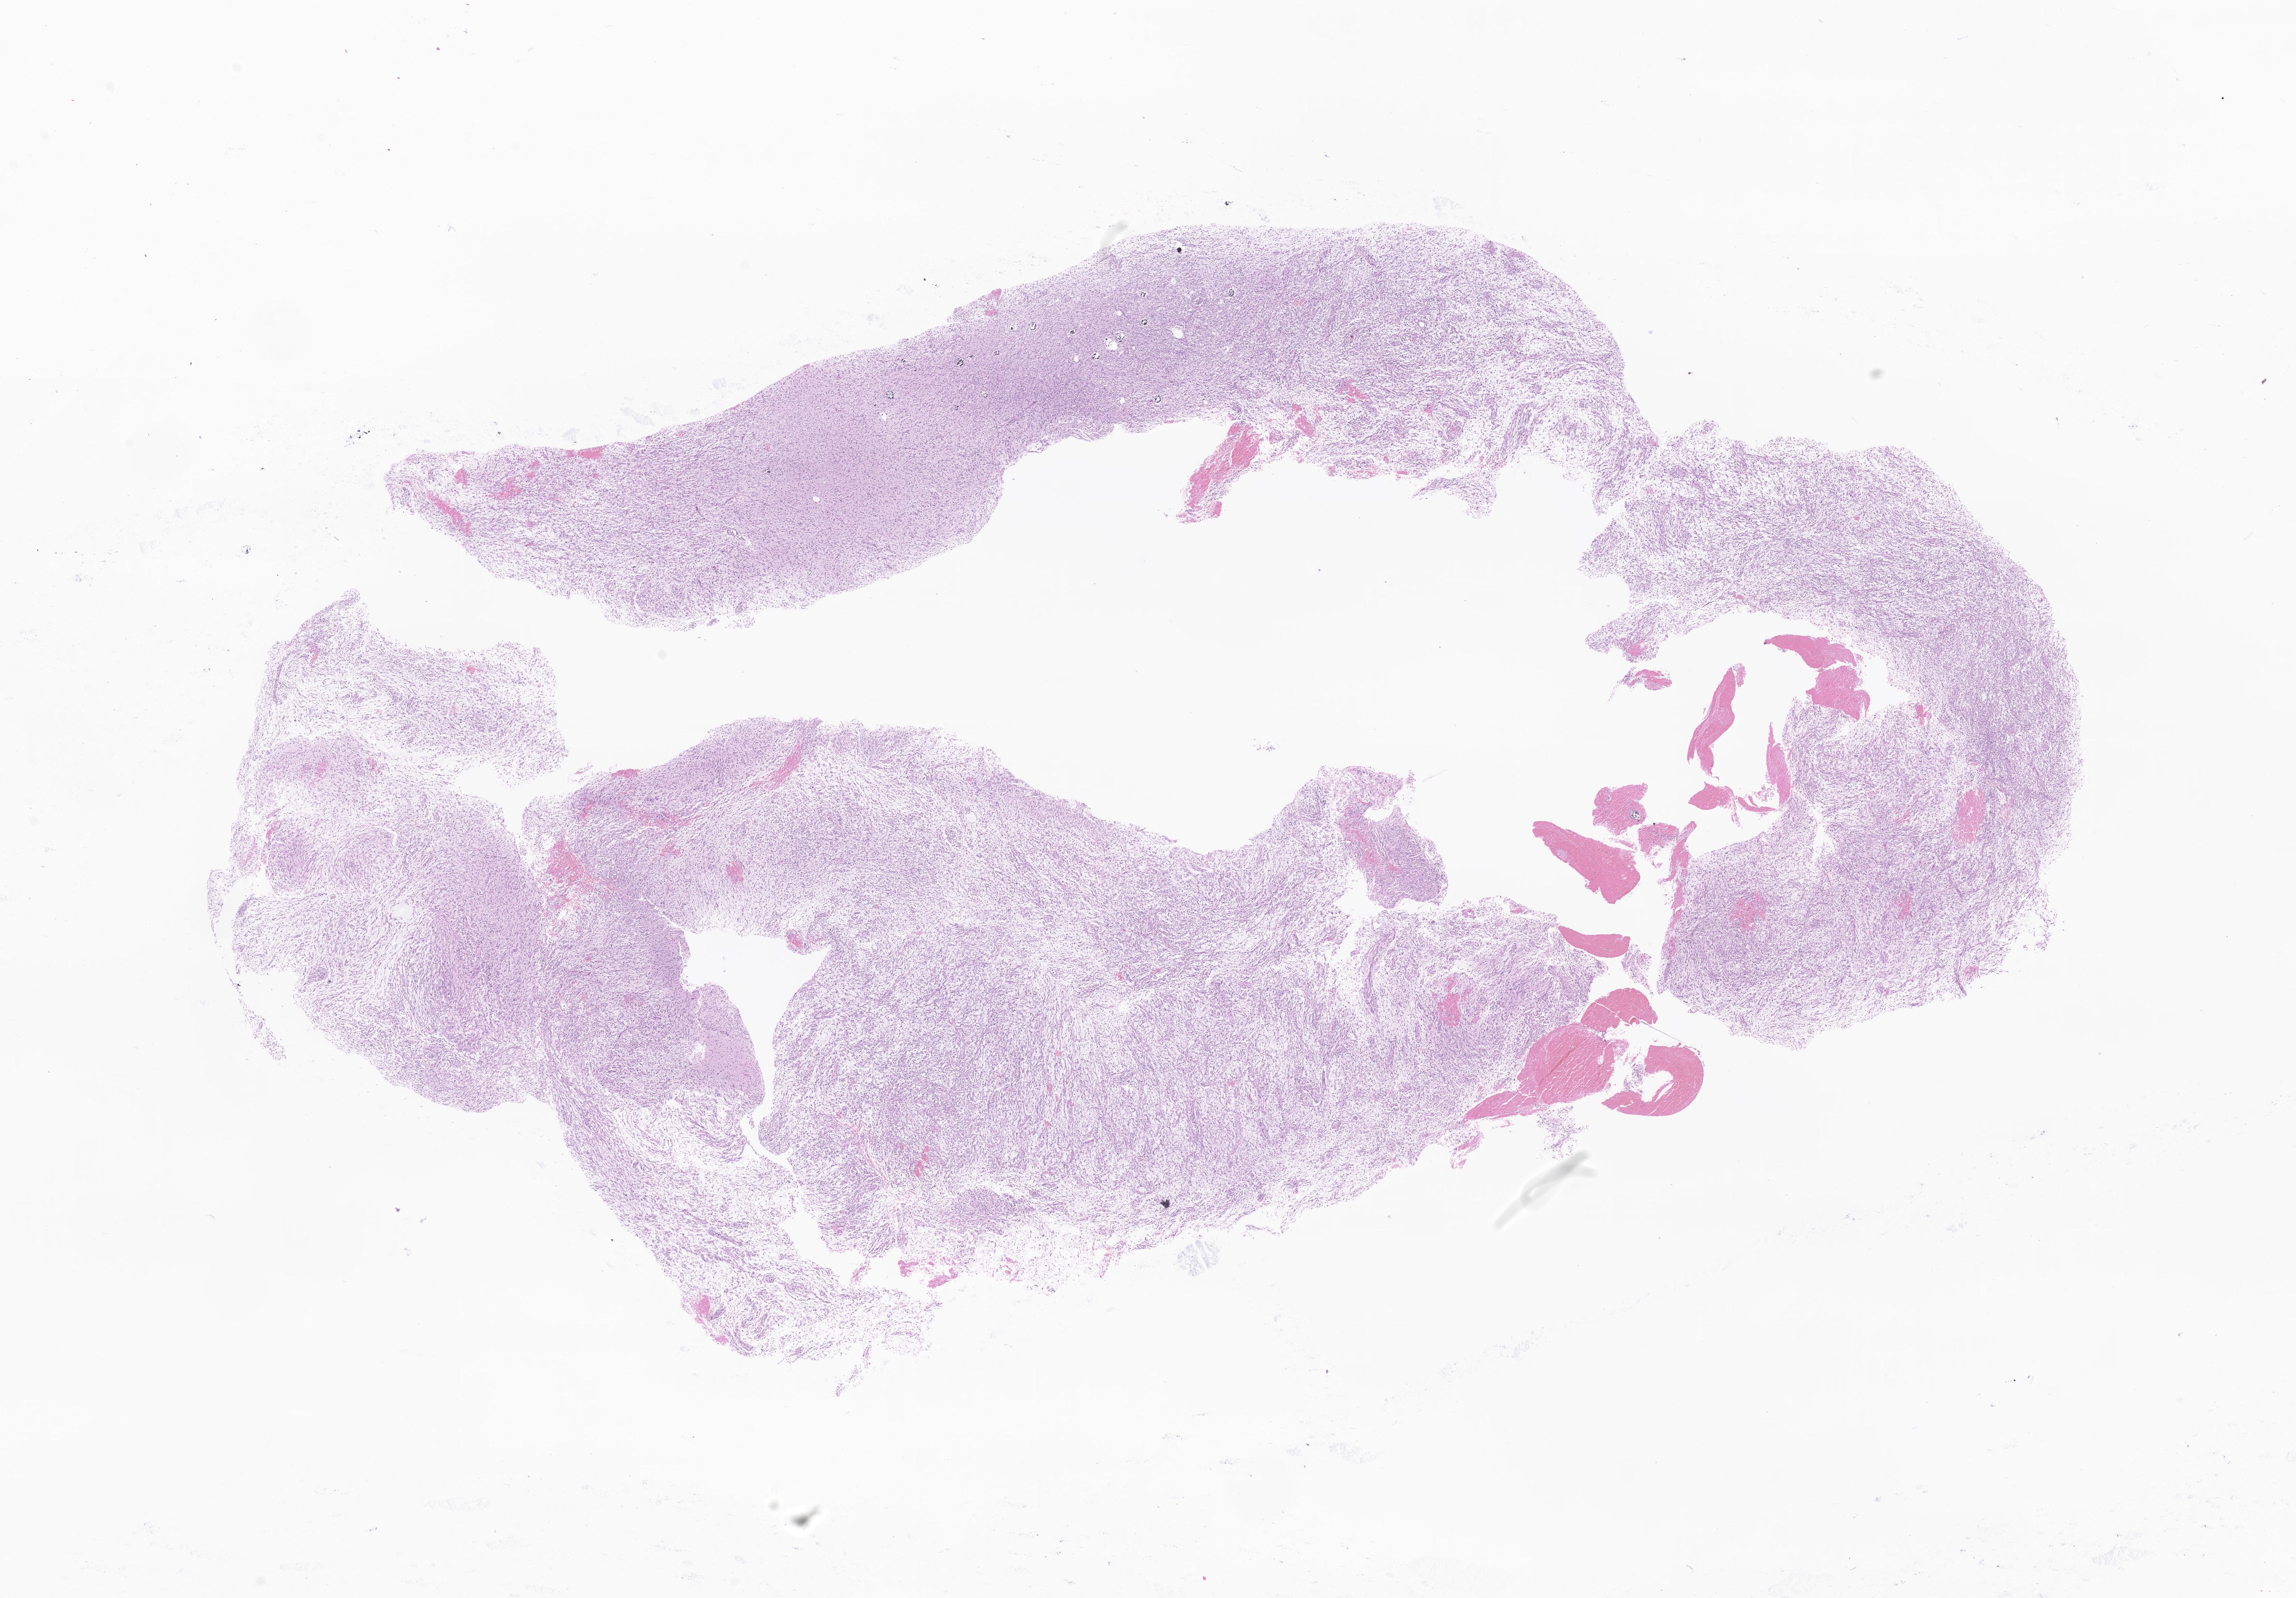
Whole-slide image, hematoxylin and eosin (H&E) stain of tumor tissue from the temporal lobe — low-resolution overview of the scanned area, about 20.0 x 13.9 mm, formalin-fixed, paraffin-embedded (FFPE) tissue. Female patient, age 765 days (about 2.1 years).
Diagnosis (ICD-O-3 morphology term): Astrocytoma, NOS.